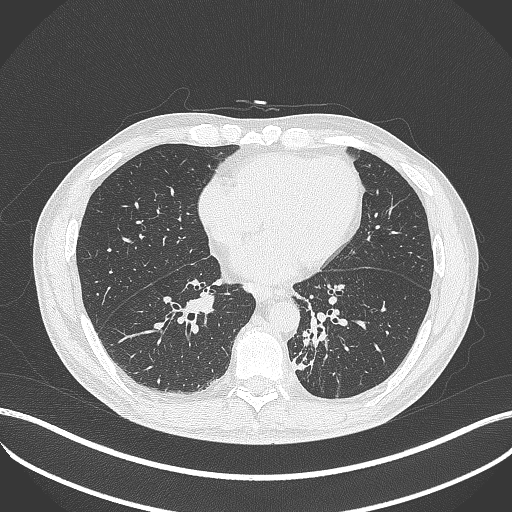
Chest CT, one axial slice. Slice 156 of 451 in the series (ordered by position). Reconstruction kernel B70f. Lung window (W 1500 / L -600 HU). 1 mm slice thickness. 512 × 512 image matrix, field of view 400 × 400 mm. Male patient, age 72 years. From the clinical record (not read from this slice): clinical TNM (as recorded): T2b N0 M1.
Outlined on this slice (bounding box drawn by a radiologist):
- lung tumour (recorded histology: adenocarcinoma): bounding box <294,328,324,376> (left, top, right, bottom; pixels)